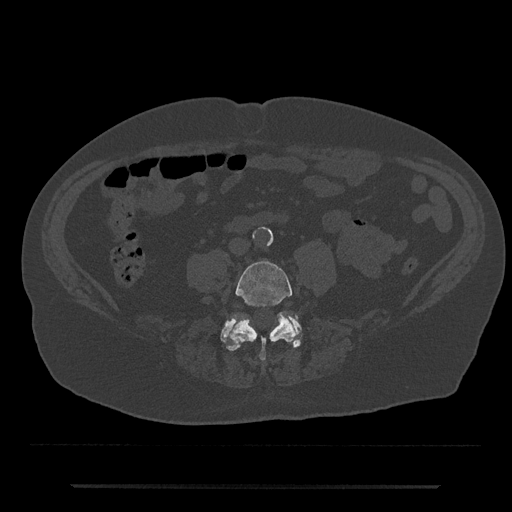
CT including the spine, one axial slice; slice 335 of 797 in the series (ordered by position); reconstruction kernel Br40s/3; bone window (W 1800 / L 400 HU); 0.5 mm slice thickness; 512 × 512 image matrix, field of view 434 × 434 mm. Male patient, age 80 years. Case-level facts recorded for this patient, not image findings: primary cancer: prostate; vertebrae with lytic lesions (as recorded): L1, T11.
Outlined on this slice (semi-automatic segmentation, software-assisted and operator-edited):
- L4 vertebra: box from (x=227, y=261) to (x=297, y=360) px
- L5 vertebra: (x=220, y=314)–(x=302, y=351)